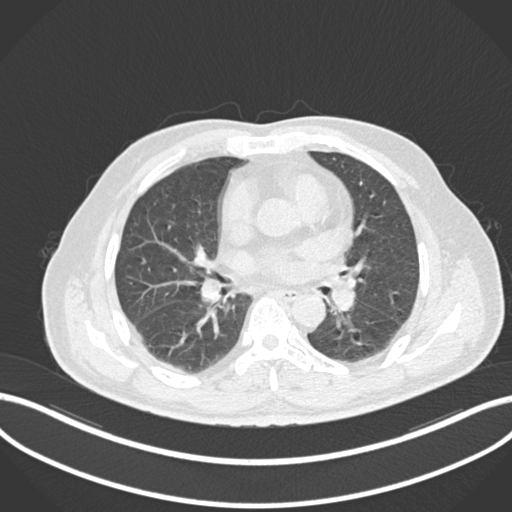
Chest CT, one axial slice; slice 70 of 161 in the series (ordered by position); 120 kVp; lung window (W 1500 / L -600 HU); 1 mm slice thickness; 512 × 512 image matrix. Male patient, age 71 years. From the clinical record (not read from this slice): clinical TNM (as recorded): T1b N0 M0.
Structures marked on this image (rectangle marked by the reading radiologist):
- lung tumour (recorded histology: squamous cell carcinoma): bounding box <329,274,358,312> (left, top, right, bottom; pixels)